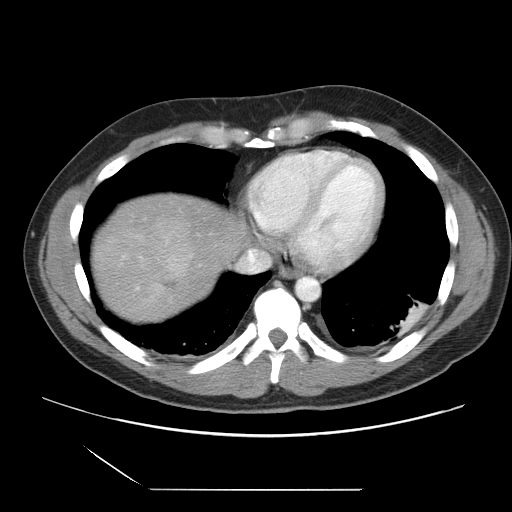
Contrast-enhanced abdominal CT, one axial slice. Slice 31 of 39 in the series (ordered by position). 120 kVp. Soft-tissue window (W 400 / L 40 HU). 512 × 512 image matrix, field of view 395 × 395 mm. Male patient, age 39 years. Case-level facts recorded for this patient, not image findings: diagnosis: colorectal cancer liver metastases, imaged before liver resection.
Structures marked on this image (expert manual segmentation):
- liver: box from (x=91, y=191) to (x=244, y=324) px
- planned liver remnant (the part of the liver to remain after resection): (x=158, y=191)–(x=243, y=240)
- liver metastasis: (x=163, y=279)–(x=179, y=290)